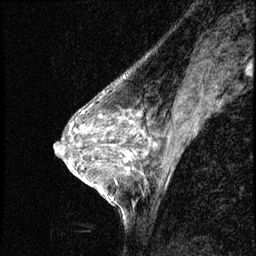
Breast MRI (dynamic contrast-enhanced), one sagittal slice. Slice 30 of 56 in the series (ordered by position). Dynamic contrast-enhanced series, image 2 of 3 at this slice position (ordered by acquisition). 1.5 T. TE 4.2 ms, TR 8.7 ms. 2.5 mm slice thickness. 256 × 256 image matrix, field of view 180 × 180 mm. Female patient, age 50 years. Case-level facts recorded for this patient, not image findings: setting: breast cancer imaged before/during neoadjuvant chemotherapy; receptor status: HR-positive, HER2-negative.
Annotated regions visible in this slice (semi-automatic segmentation, software-assisted and operator-edited):
- analysis volume of interest (the breast-tissue region the enhancement analysis was run in; not a lesion): box from (x=119, y=136) to (x=169, y=190) px
- tumour enhancement mask (voxels above the 140 % enhancement threshold inside the analysis volume of interest): (x=127, y=144)–(x=155, y=156)